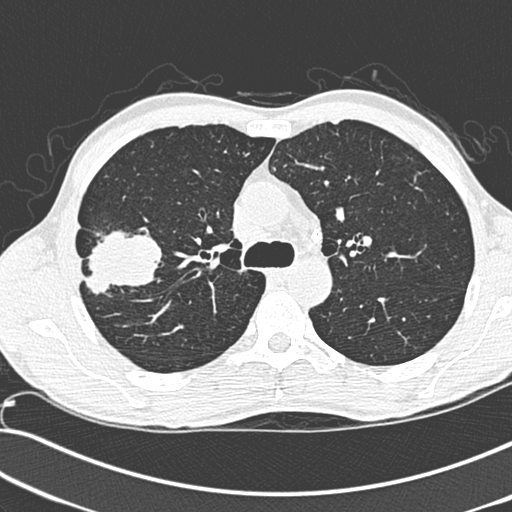
Low-dose screening chest CT, one axial slice. Slice 203 of 281 in the series (ordered by position). 120 kVp. Lung window (W 1500 / L -600 HU). 1.3 mm slice thickness. 512 × 512 image matrix, field of view 341 × 341 mm.
Annotated regions visible in this slice (expert manual segmentation):
- lesion 1 (tumor, upper lobe of right lung): bounding box <85,229,164,298> (left, top, right, bottom; pixels)